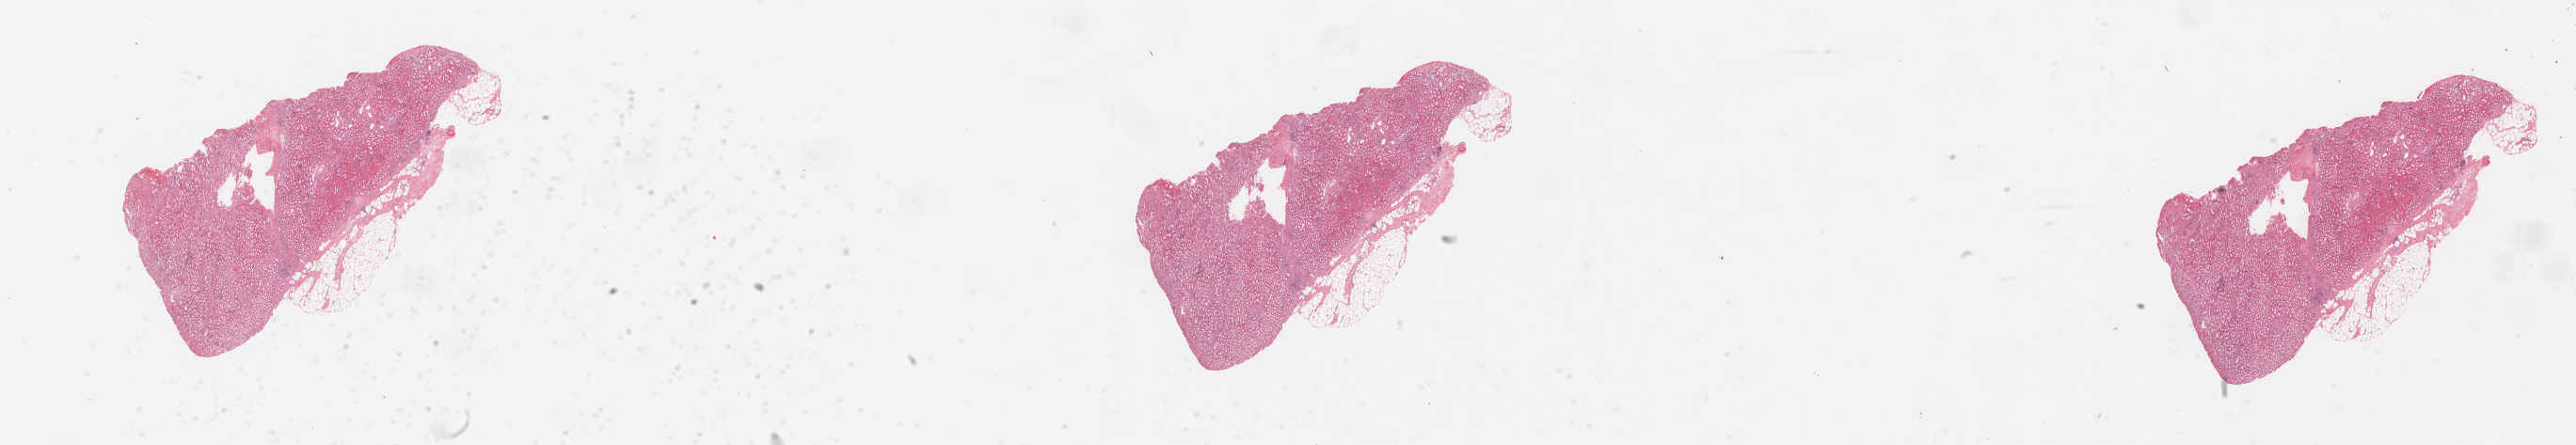
Digitized H&E tissue section (whole slide) — whole scanned area (about 43.3 x 7.5 mm, from a 20x scan) shown as a low-resolution overview; normal (non-tumour) tissue sample, sampled site: kidney. 51-year-old female patient.
This section: normal (non-tumour) tissue from the same patient. Patient diagnosis: Renal cell carcinoma, NOS.